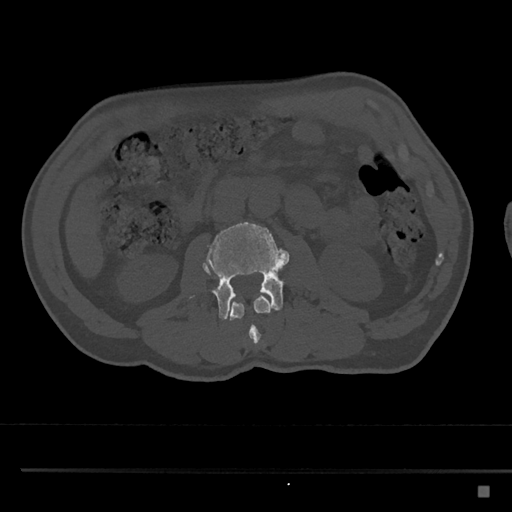
CT including the spine, one axial slice. Slice 719 of 797 in the series (ordered by position). Bone window (W 1800 / L 400 HU). 512 × 512 image matrix, field of view 391 × 391 mm. Male patient, age 59 years. Case-level facts recorded for this patient, not image findings: primary cancer: prostate.
Annotated regions visible in this slice (semi-automatically segmented with operator editing):
- L2 vertebra: box from (x=206, y=270) to (x=273, y=345) px
- L3 vertebra: (x=188, y=221)–(x=289, y=320)